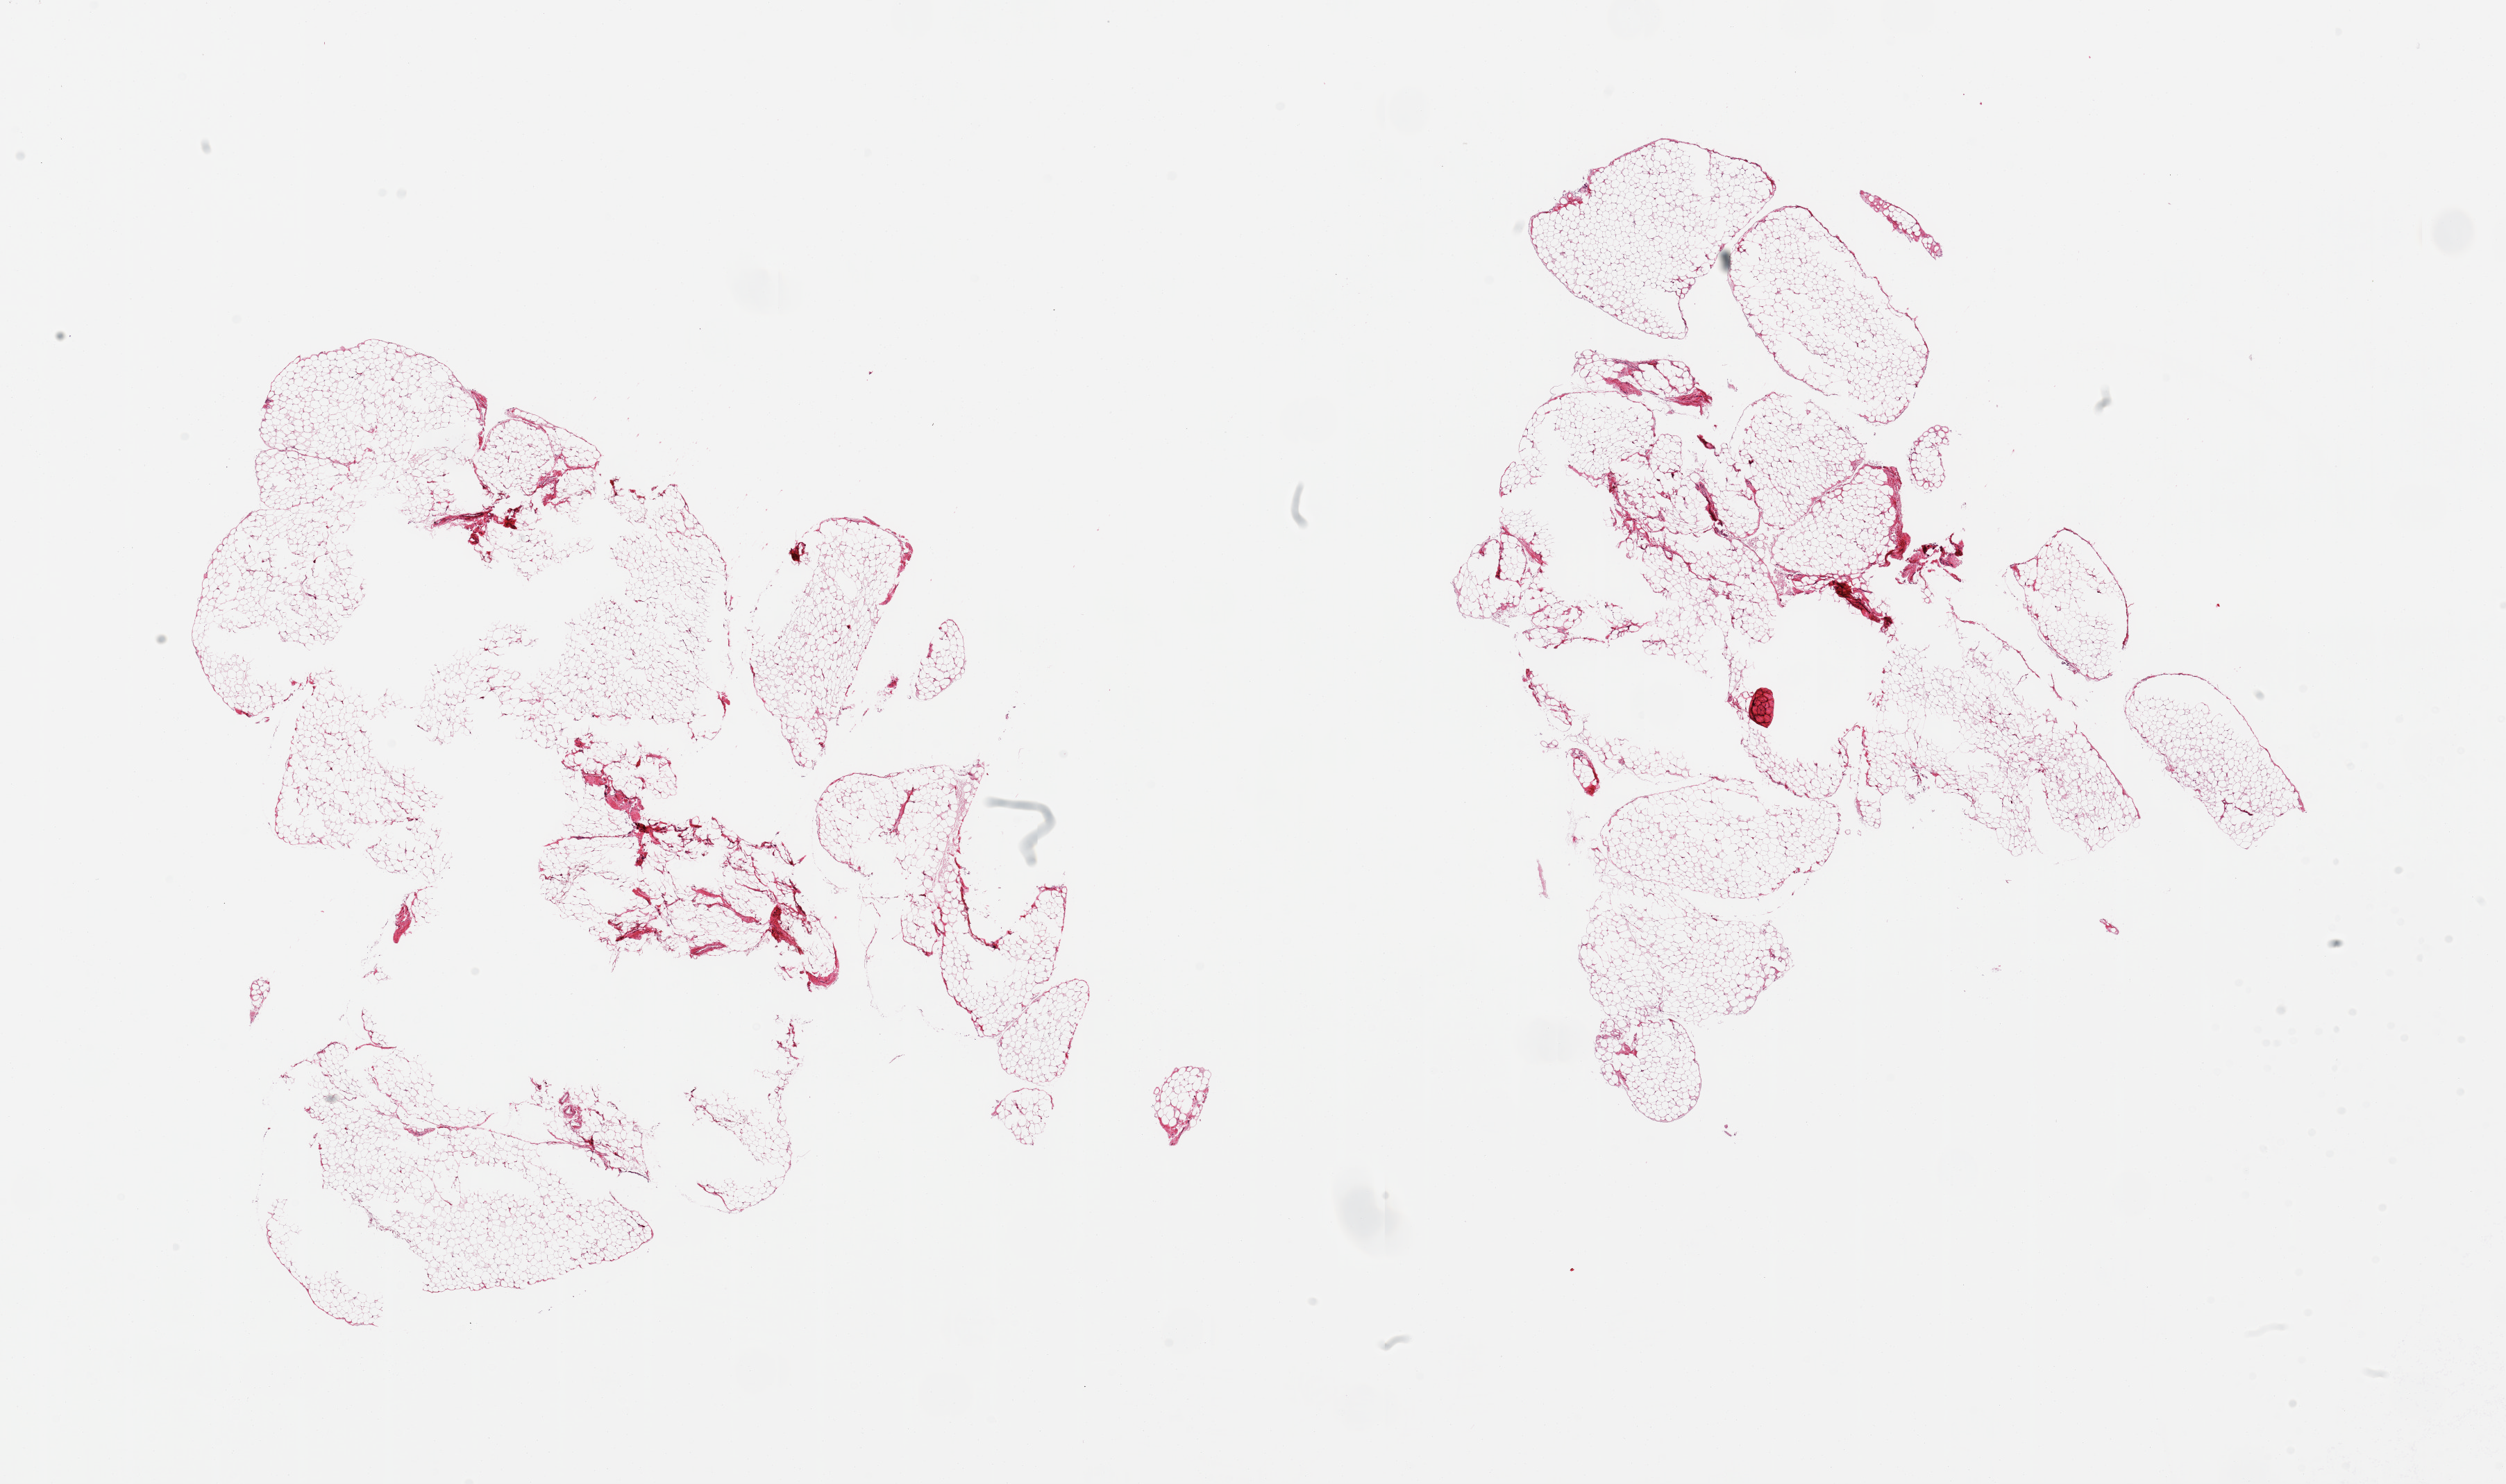
H&E whole-slide image, brightfield, low-resolution overview of the scanned area, about 28.5 x 16.9 mm (acquisition: 20x scan). PAXgene-fixed paraffin-embedded (PFPE) section. Sampled site (target tissue): omentum. Tissue donor sample. Male donor.
Review note (as recorded): 2 pieces, trace fascia/vascular elements.